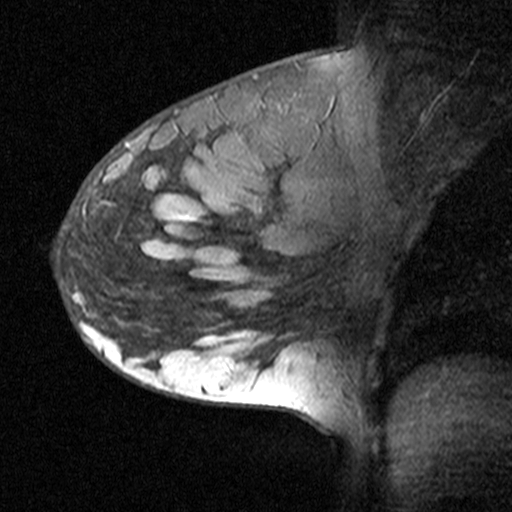
Breast MRI (dynamic contrast-enhanced), one sagittal slice. Slice 27 of 44 in the series (ordered by position). Dynamic contrast-enhanced study with each time point stored as its own series, time point 2 of 3 at this slice position (early post-contrast, ordered by acquisition time). 1.5 T. TE 4.5 ms, TR 11 ms. 512 × 512 image matrix, field of view 200 × 200 mm. Female patient, age 27 years. From the clinical record (not read from this slice): setting: breast cancer imaged before/during neoadjuvant chemotherapy; receptor status: HR-positive, HER2-negative.
Outlined on this slice (semi-automatic segmentation, software-assisted and operator-edited):
- analysis volume of interest (the breast-tissue region the enhancement analysis was run in; not a lesion): bounding box [x1, y1, x2, y2] px = [54, 162, 163, 271]
- tumour enhancement mask (voxels above the 90 % enhancement threshold inside the analysis volume of interest): [83, 169, 149, 209]